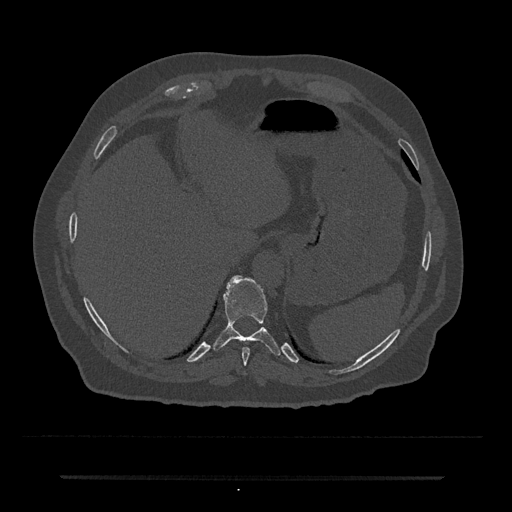
CT including the spine, one axial slice. Slice 237 of 797 in the series (ordered by position). Reconstruction kernel Br40s/3. 120 kVp. Bone window (W 1800 / L 400 HU). 512 × 512 image matrix, field of view 437 × 437 mm. Patient: male, 69 years. From the clinical record (not read from this slice): primary cancer: prostate.
Annotated regions visible in this slice (semi-automatically segmented with operator editing):
- T10 vertebra: box from (x=213, y=276) to (x=281, y=355) px
- T9 vertebra: (x=242, y=347)–(x=250, y=365)